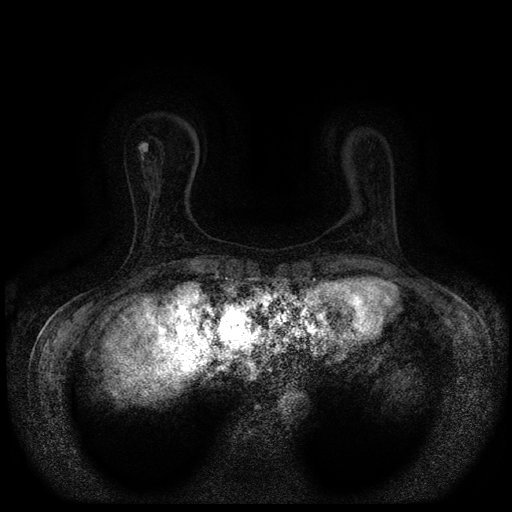
Breast MRI (dynamic contrast-enhanced, multi-phase), one axial slice; slice 21 of 116 in the series (ordered by position); dynamic contrast-enhanced series, time point 2 of 5 at this slice position (early post-contrast); 1.5 T; TE 2.7 ms, TR 5.4 ms; 2 mm slice thickness; 512 × 512 image matrix, field of view 330 × 330 mm. Female patient, age 63 years.
Structures marked on this image (semi-automatic segmentation, software-assisted and operator-edited):
- breast lesion (labelled benign in the annotation): bounding box (x1, y1, x2, y2) in pixels: (138, 141, 149, 161)